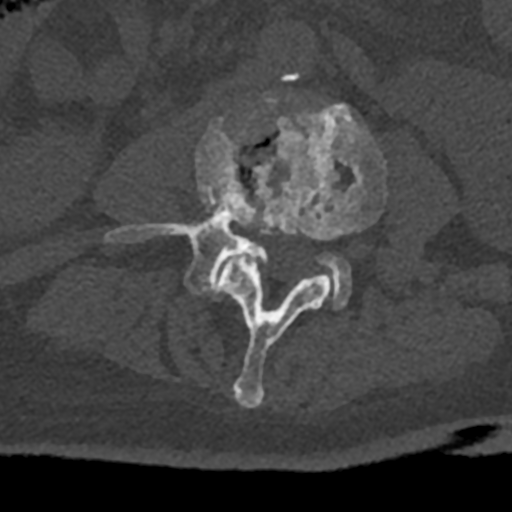
CT including the spine, one axial slice. Reconstruction kernel Br40s/3. Bone window (W 1800 / L 400 HU). 0.5 mm slice thickness. 512 × 512 image matrix, field of view 160 × 160 mm. Male patient, age 74 years. From the clinical record (not read from this slice): primary cancer: renal.
Annotated regions visible in this slice (semi-automatically segmented with operator editing):
- L3 vertebra: box from (x=220, y=100) to (x=387, y=407) px
- L4 vertebra: (x=105, y=119)–(x=351, y=309)